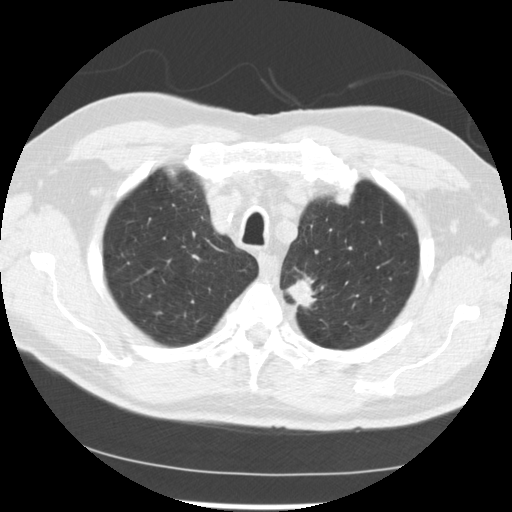
Low-dose screening chest CT, one axial slice; slice 206 of 249 in the series (ordered by position); reconstruction kernel STANDARD; lung window (W 1500 / L -600 HU); 512 × 512 image matrix, field of view 341 × 341 mm.
Outlined on this slice (outlined manually by an expert reader):
- lesion 2 (tumor, upper lobe of left lung): box from (x=287, y=279) to (x=316, y=308) px